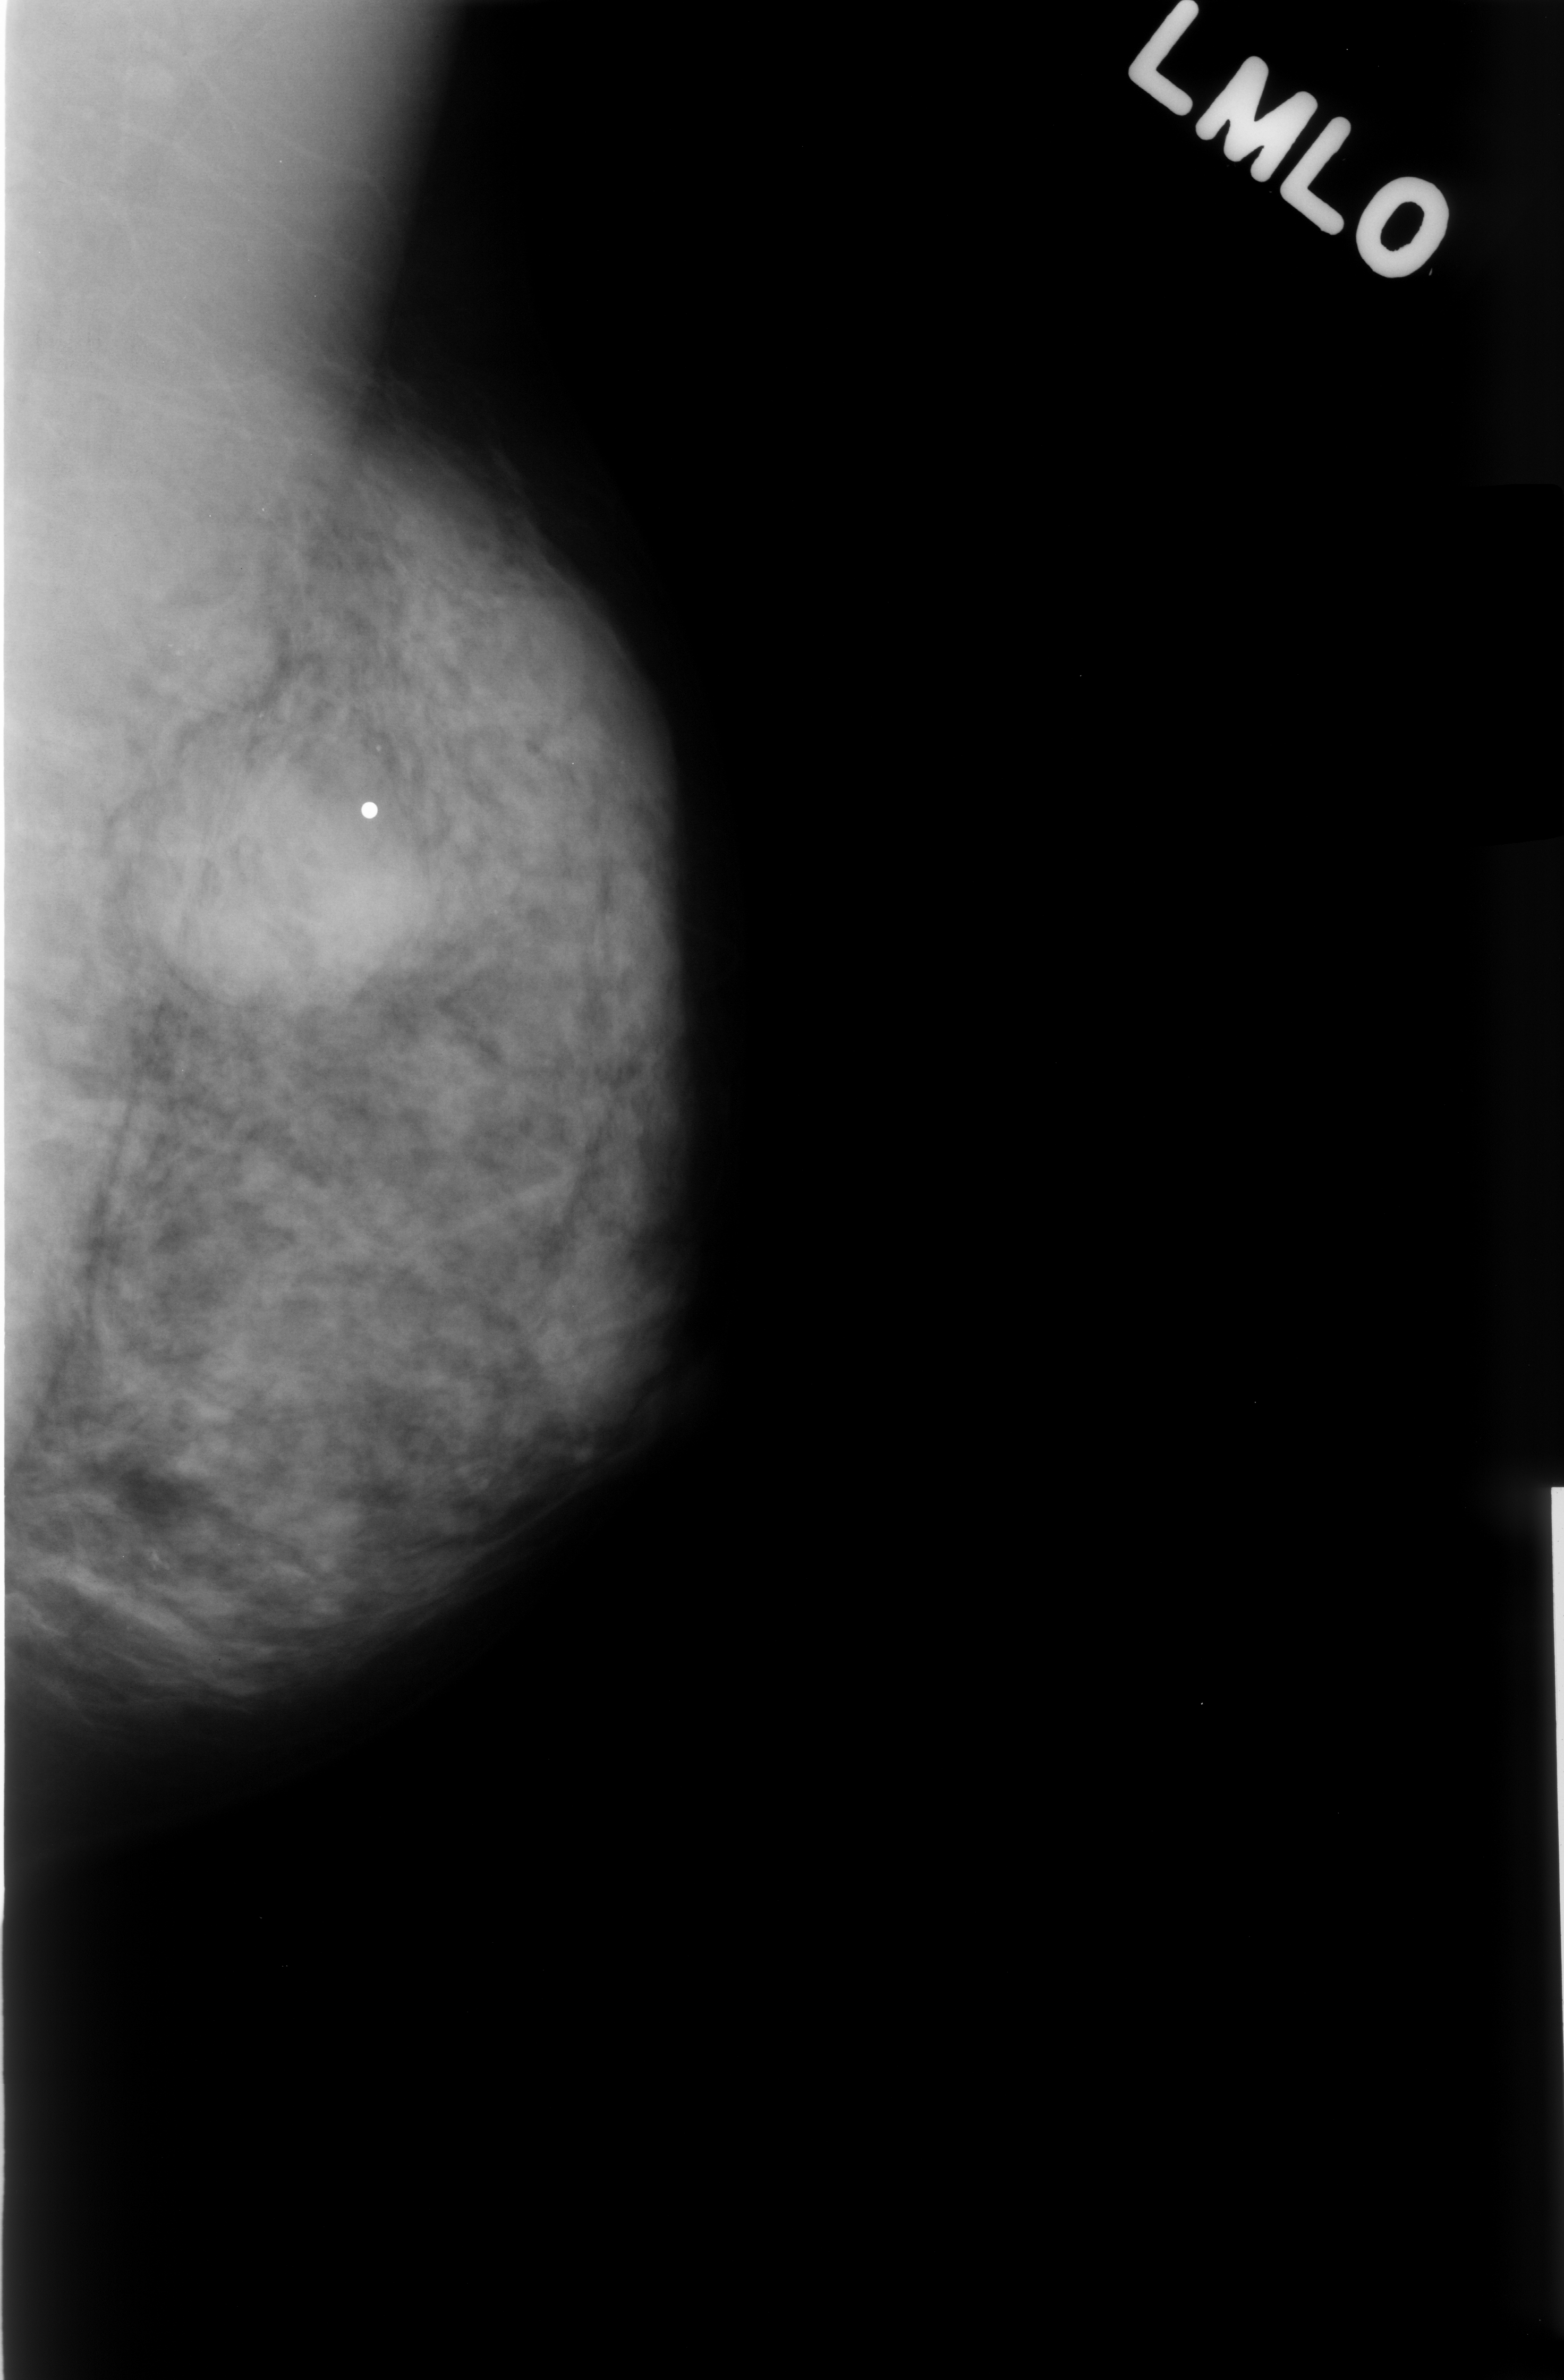
Digitized screen-film mammogram. Left breast. Mediolateral oblique (MLO) view. BI-RADS breast density category 3 (scale 1–4). 1564 × 2380 image matrix.
Marked abnormalities (boxes around the expert regions of interest):
- mass, shape round, margins microlobulated; BI-RADS assessment category 3; subtlety rating 5 on a 1 (subtle) to 5 (obvious) scale; pathology result (as recorded, not read from the image): benign: bounding box [x1, y1, x2, y2] px = [165, 746, 424, 1021]